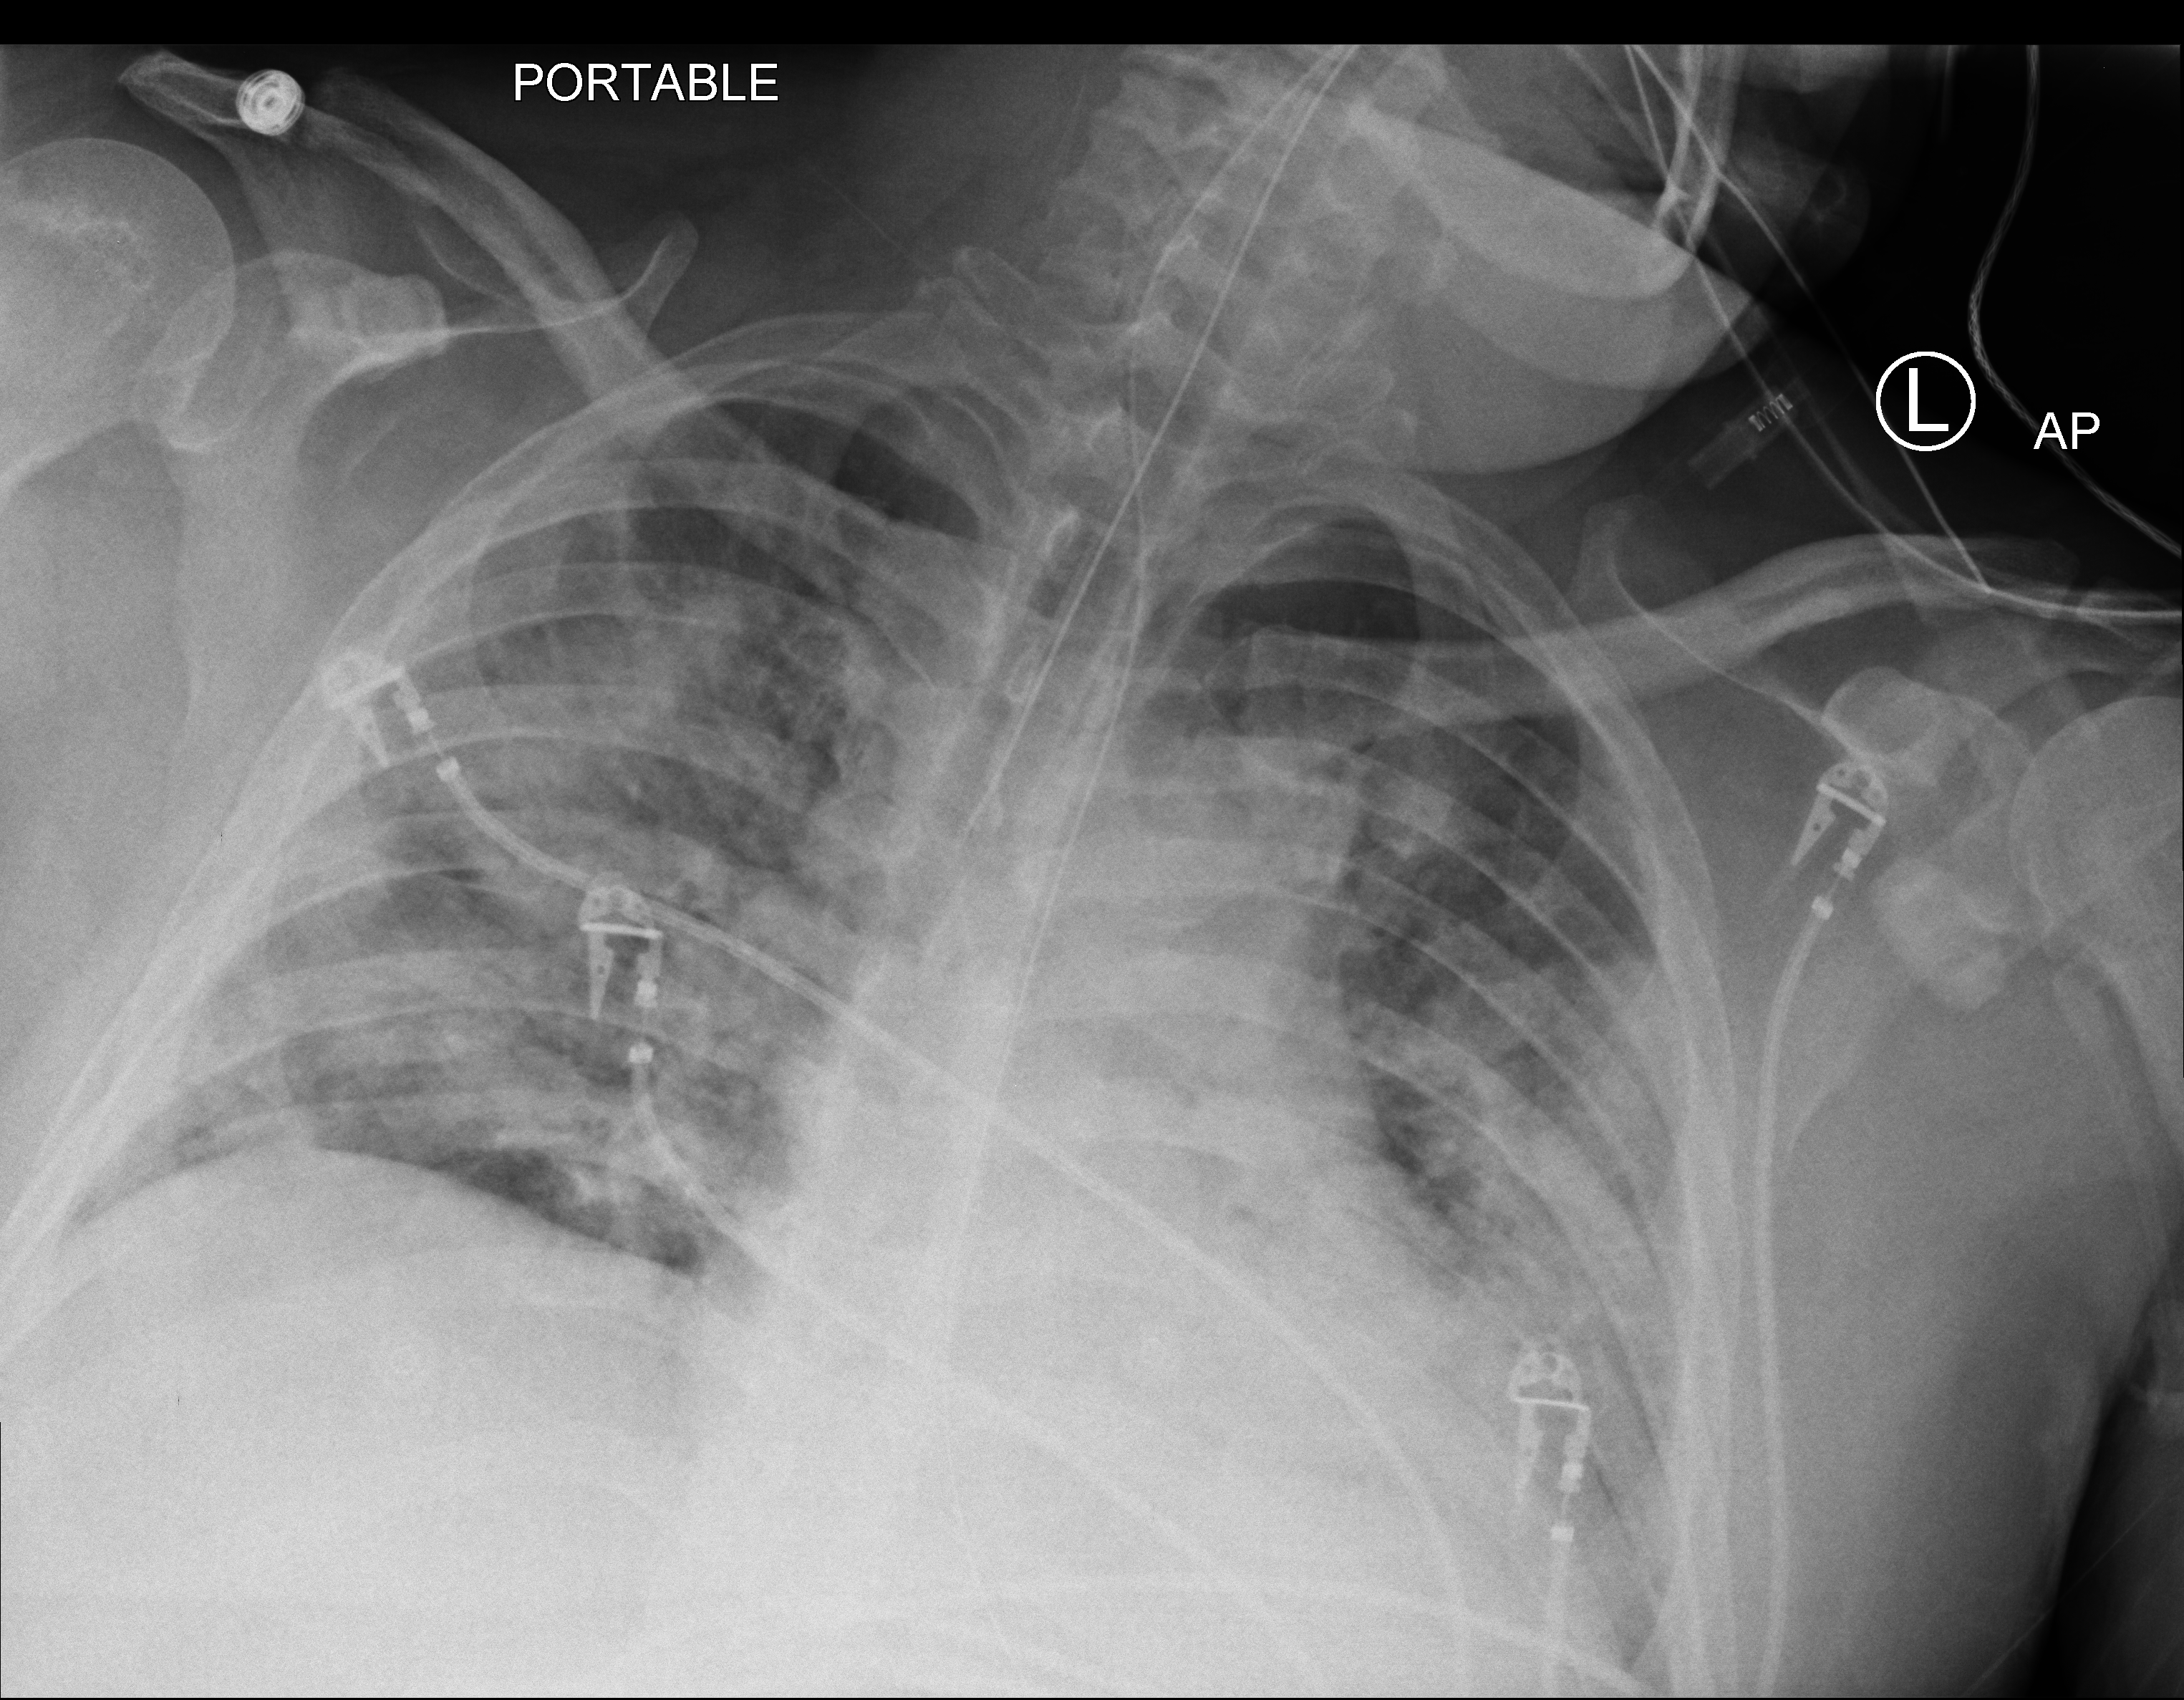
Portable chest radiograph; anteroposterior (AP) projection. Patient hospitalised with COVID-19; male, aged 18–59 years.
Admission-level facts for this patient (not findings on this image; timing relative to this image not recorded):
- COPD (admission record): no
- smoking status (admission record): never